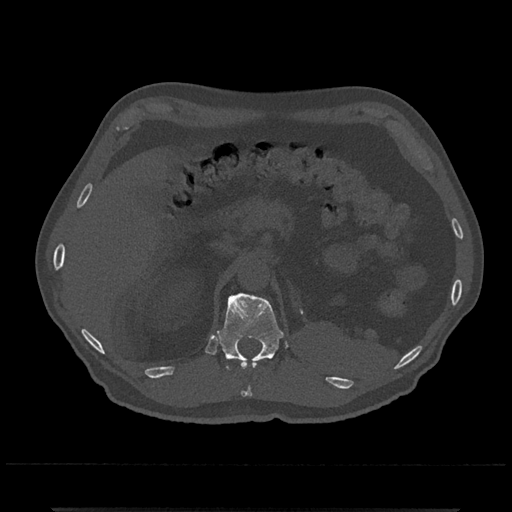
CT including the spine, one axial slice. Position 444 of 797 along the scan axis. 120 kVp. Bone window (W 1800 / L 400 HU). 0.5 mm slice thickness. 512 × 512 image matrix, field of view 393 × 393 mm. Patient: male, 67 years. Case-level facts recorded for this patient, not image findings: primary cancer: prostate.
Outlined on this slice (semi-automatic segmentation, software-assisted and operator-edited):
- T11 vertebra: bounding box <232,358,256,397> (left, top, right, bottom; pixels)
- T12 vertebra: <217,293,284,370>